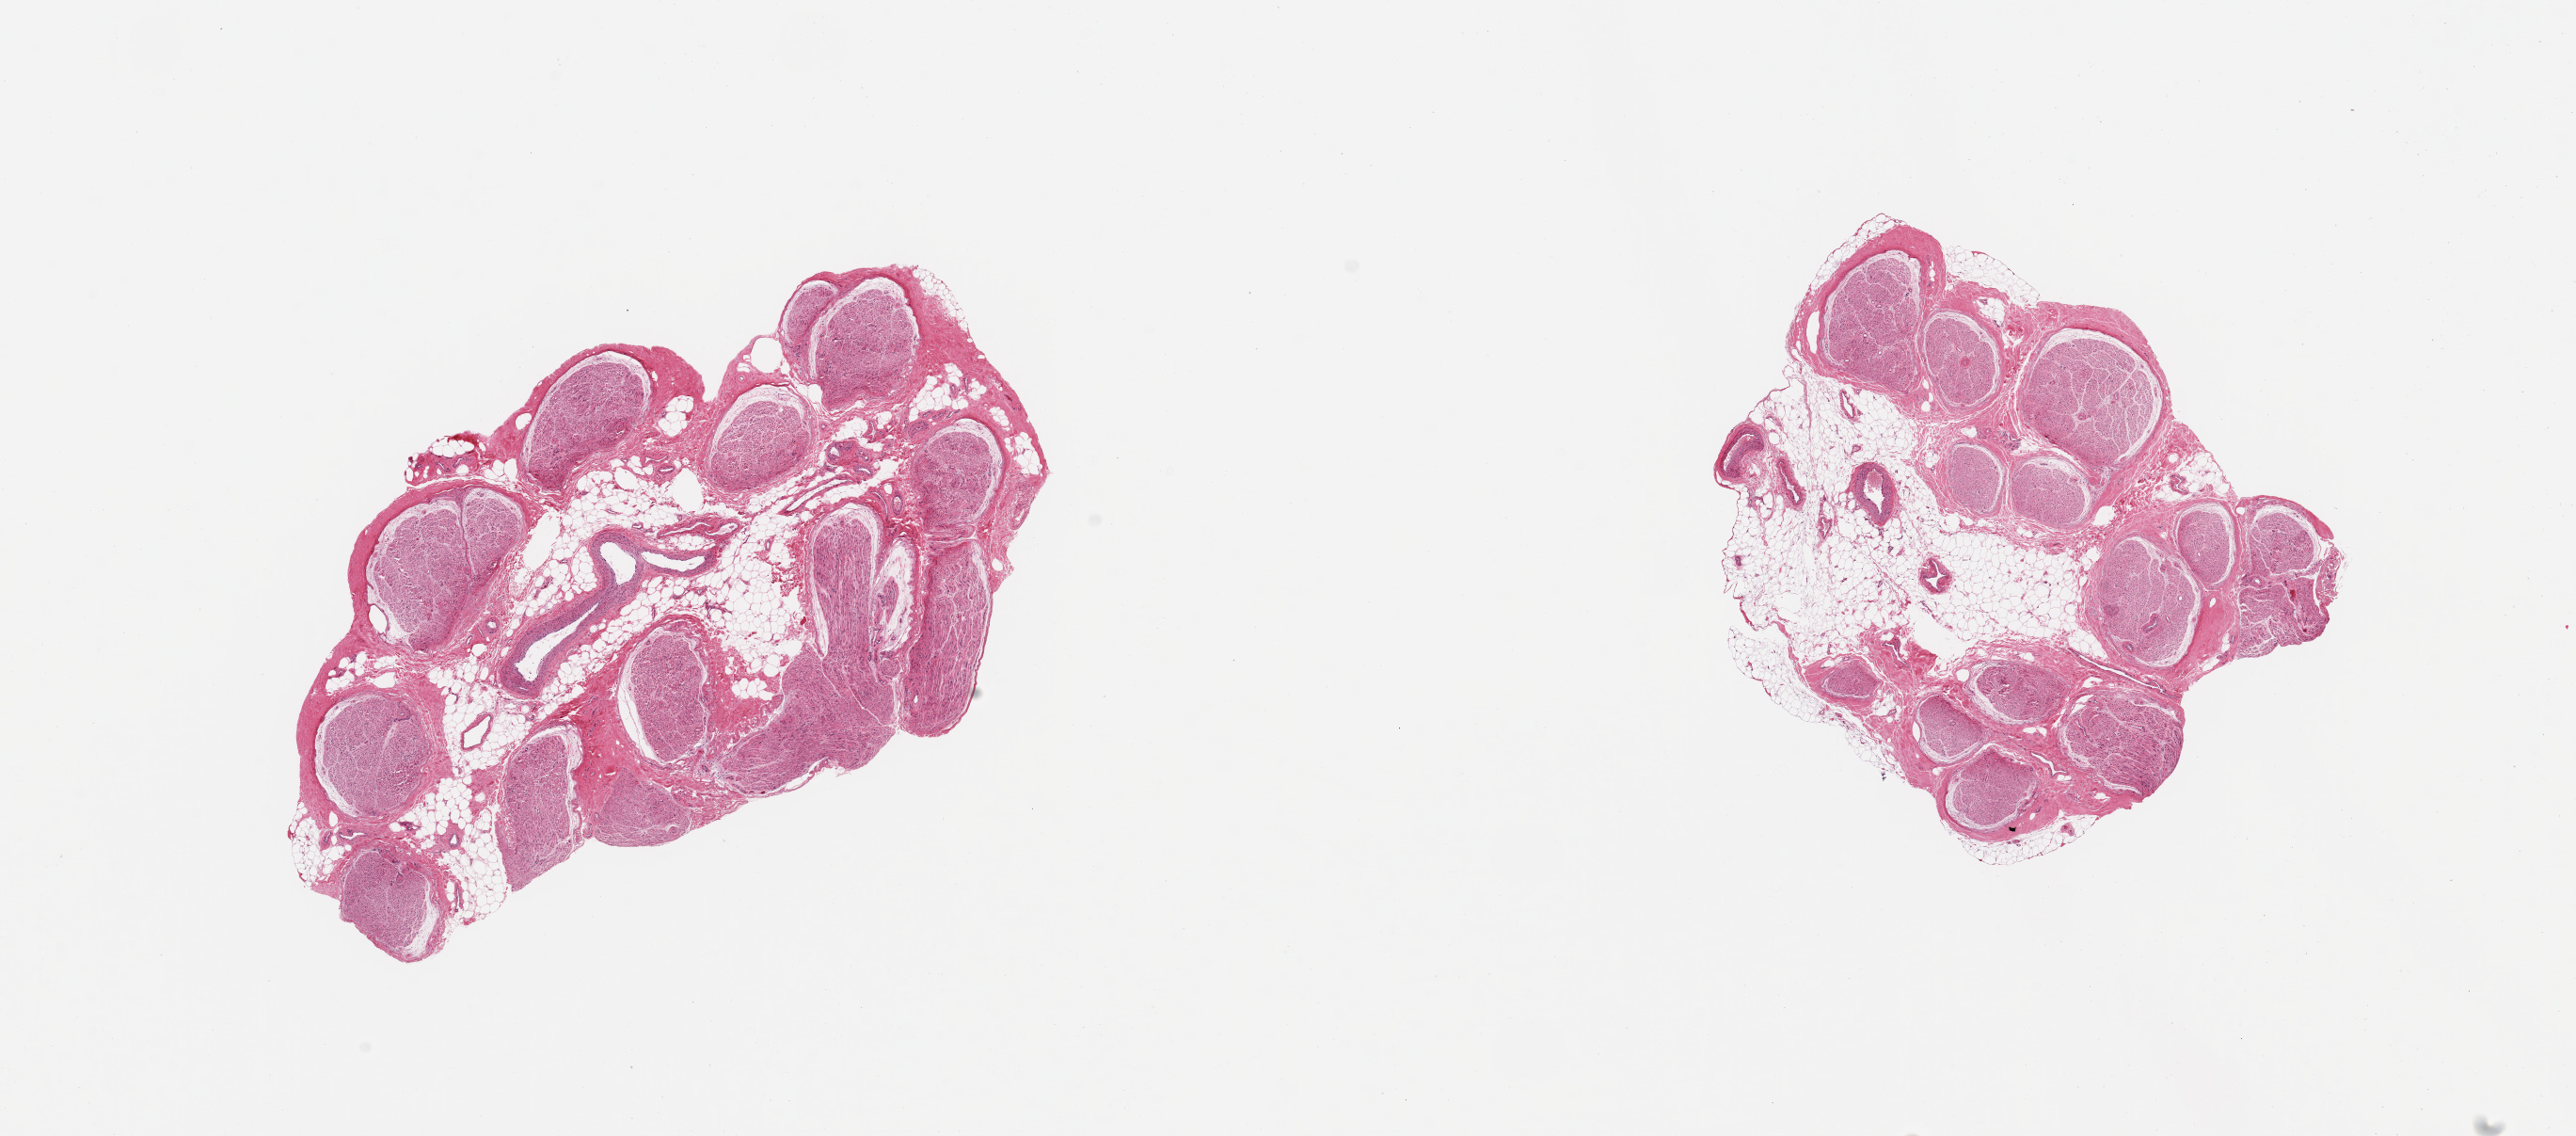
Digitized hematoxylin and eosin (H&E)-stained section, brightfield, shown as a low-resolution overview of the whole scanned area (about 21.7 x 9.5 mm, from a 20x scan); PAXgene-fixed paraffin-embedded (PFPE) section; sampled site (target tissue): tibial nerve; donor tissue sample. Male donor.
- pathologist's review note for this sample: 2 pieces; 20% and 30% predominantly internal fat